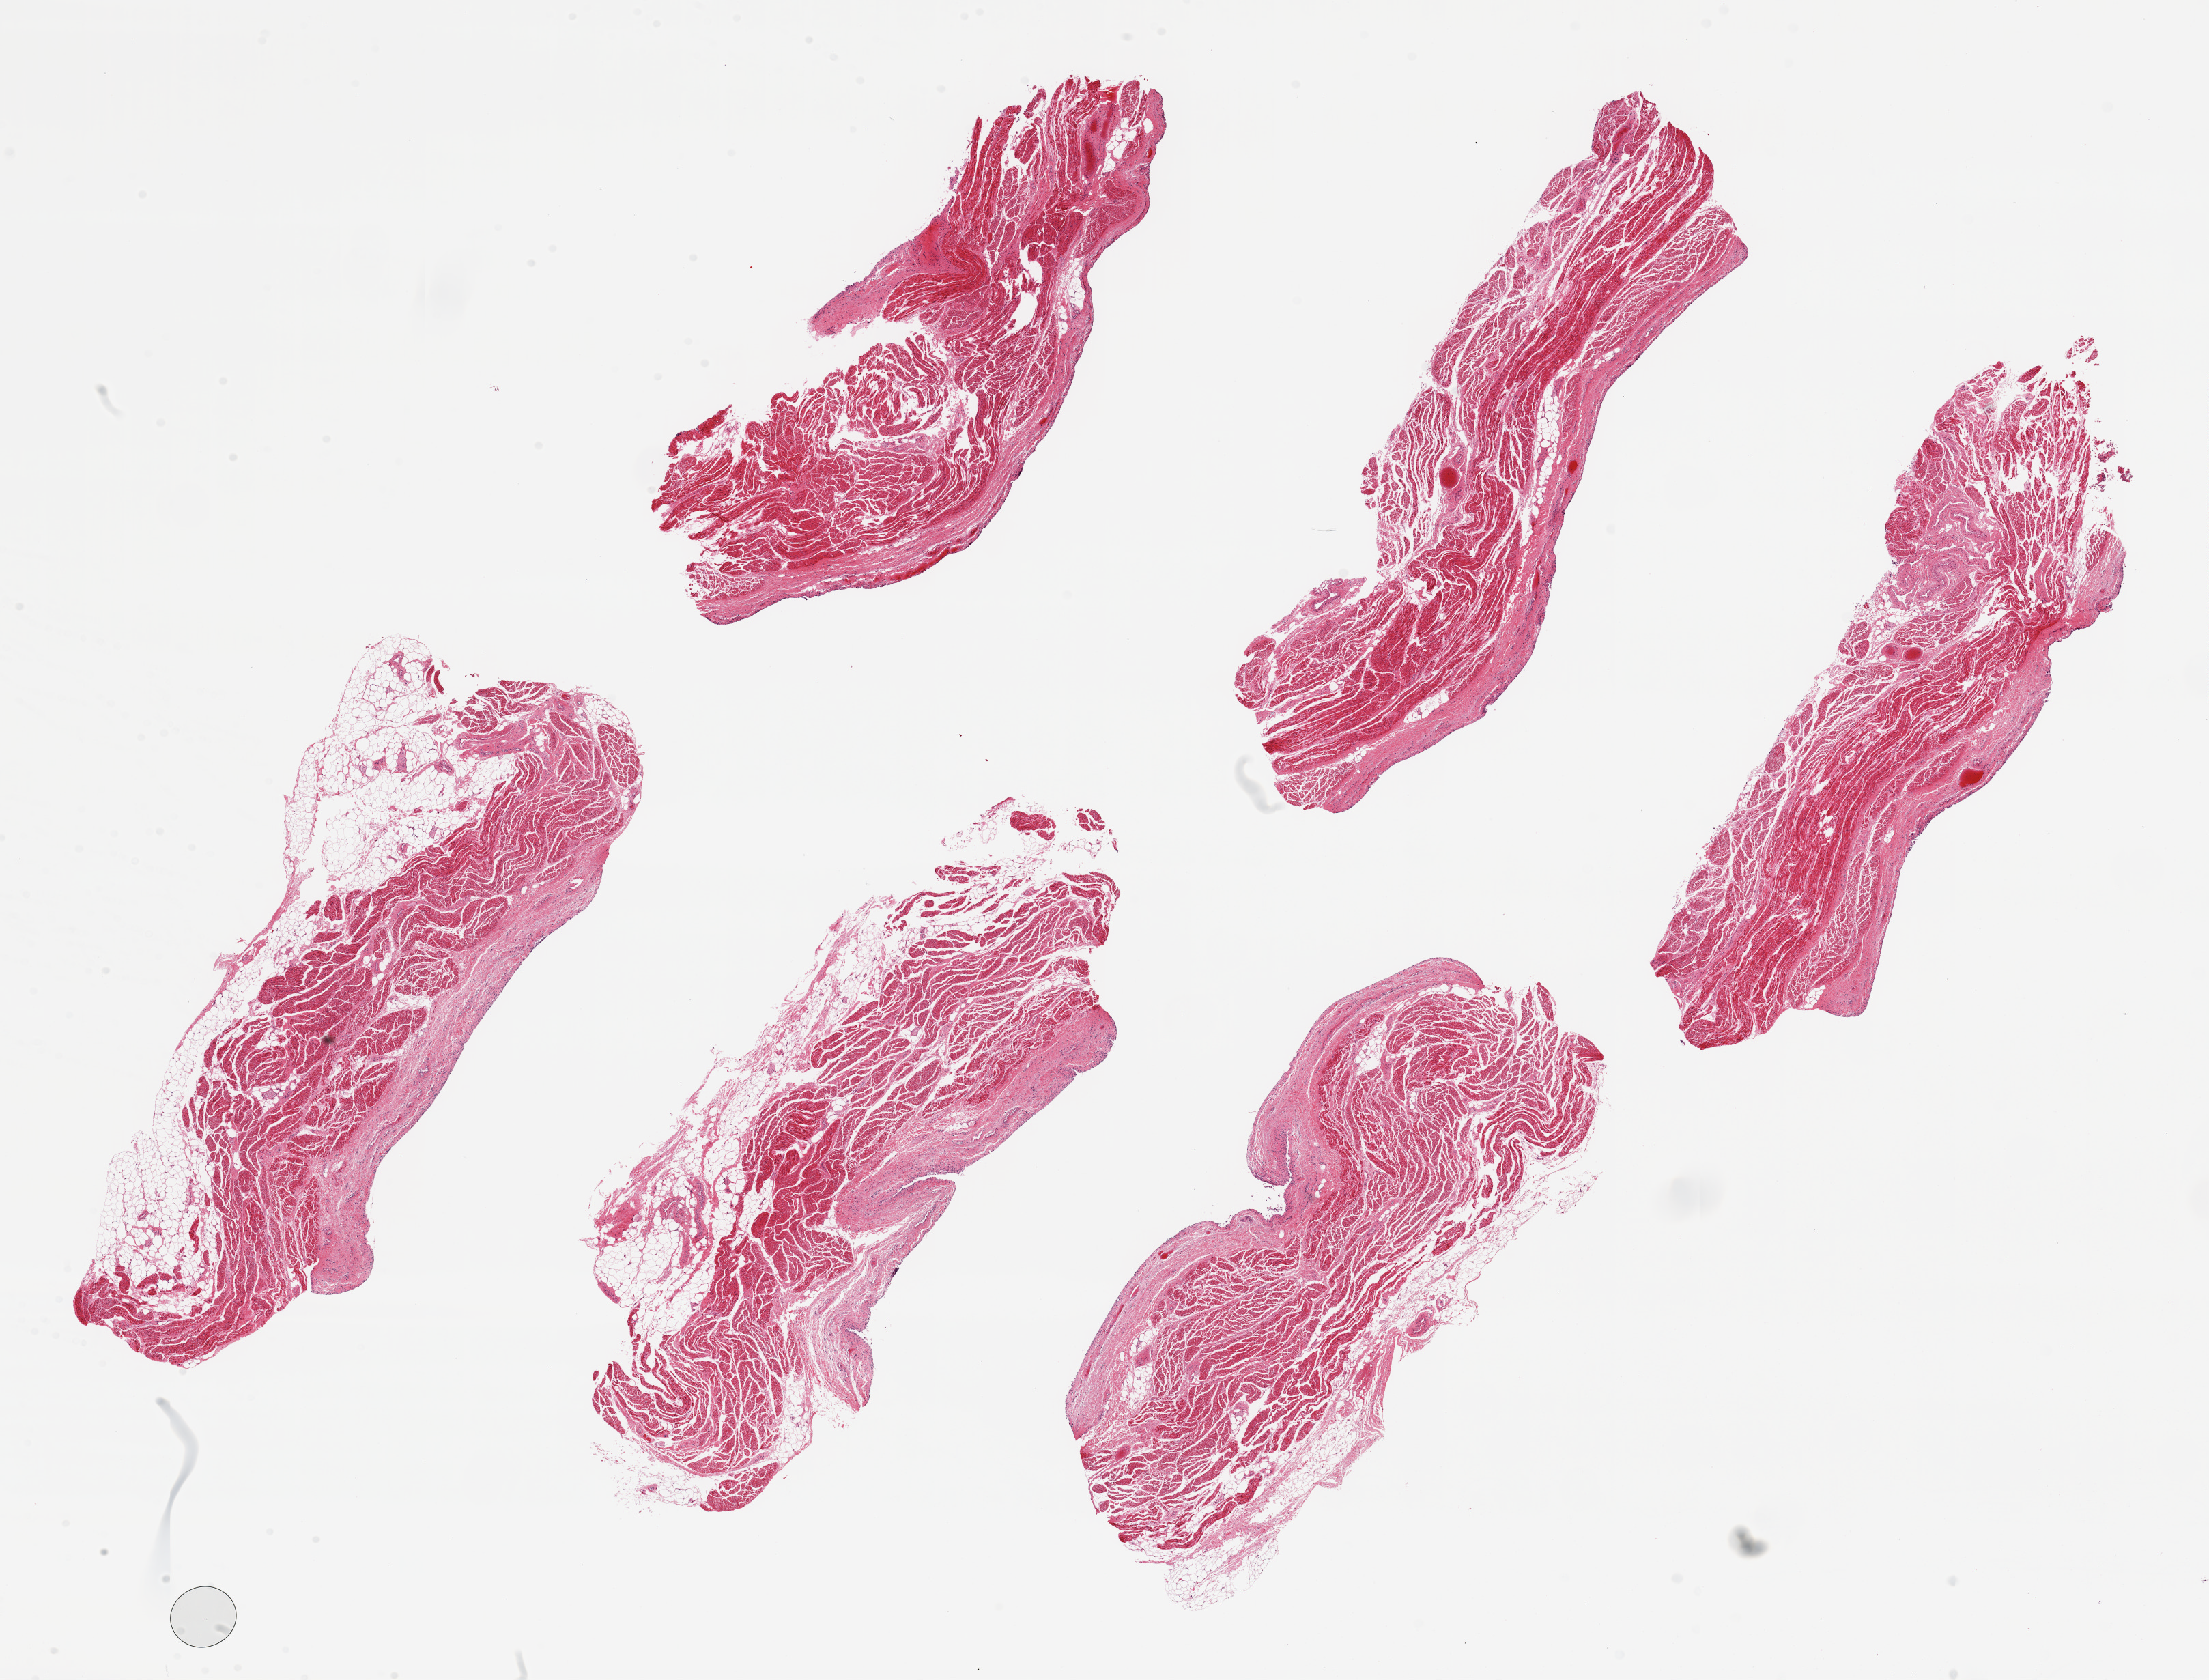
Digitized H&E-stained section — a low-resolution overview of the entire scanned area, about 25.6 x 19.5 mm; PAXgene-fixed, paraffin-embedded tissue; sampled site (target tissue): urinary bladder; donor tissue sample. Donor: male.
Pathologist's review note for this sample: 6 pieces, ~8x3mm. Urothelium totally sloughed.